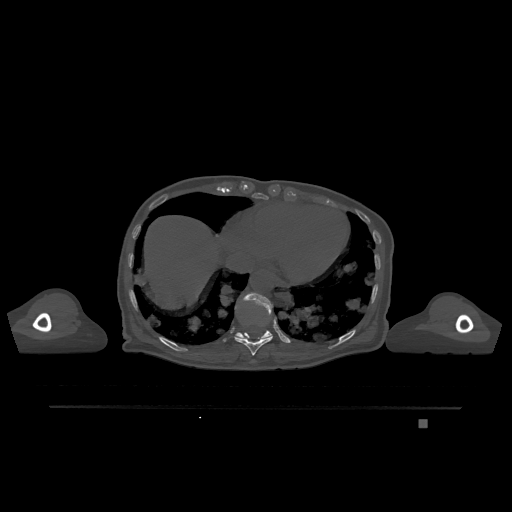
CT including the spine, one axial slice. Bone window (W 1800 / L 400 HU). 512 × 512 image matrix. Patient: female, 74 years. Case-level facts recorded for this patient, not image findings: primary cancer: lung.
Structures marked on this image (semi-automatic segmentation, software-assisted and operator-edited):
- T10 vertebra: box from (x=234, y=333) to (x=273, y=356) px
- T11 vertebra: (x=235, y=293)–(x=273, y=339)